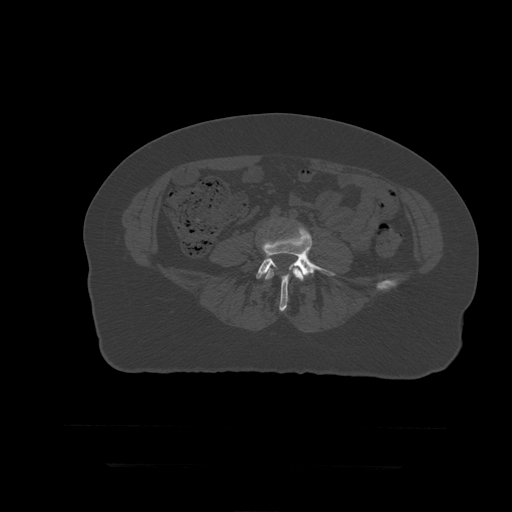
CT including the spine, one axial slice. Position 81 of 399 along the scan axis. Reconstruction kernel STANDARD. Bone window (W 1800 / L 400 HU). 1.25 mm slice thickness. 512 × 512 image matrix, field of view 450 × 450 mm. Patient age 41 years. From the clinical record (not read from this slice): primary cancer: breast.
Annotated regions visible in this slice (semi-automatically segmented with operator editing):
- L4 vertebra: bounding box (x1, y1, x2, y2) in pixels: (265, 261, 304, 296)
- L5 vertebra: (256, 227, 336, 312)